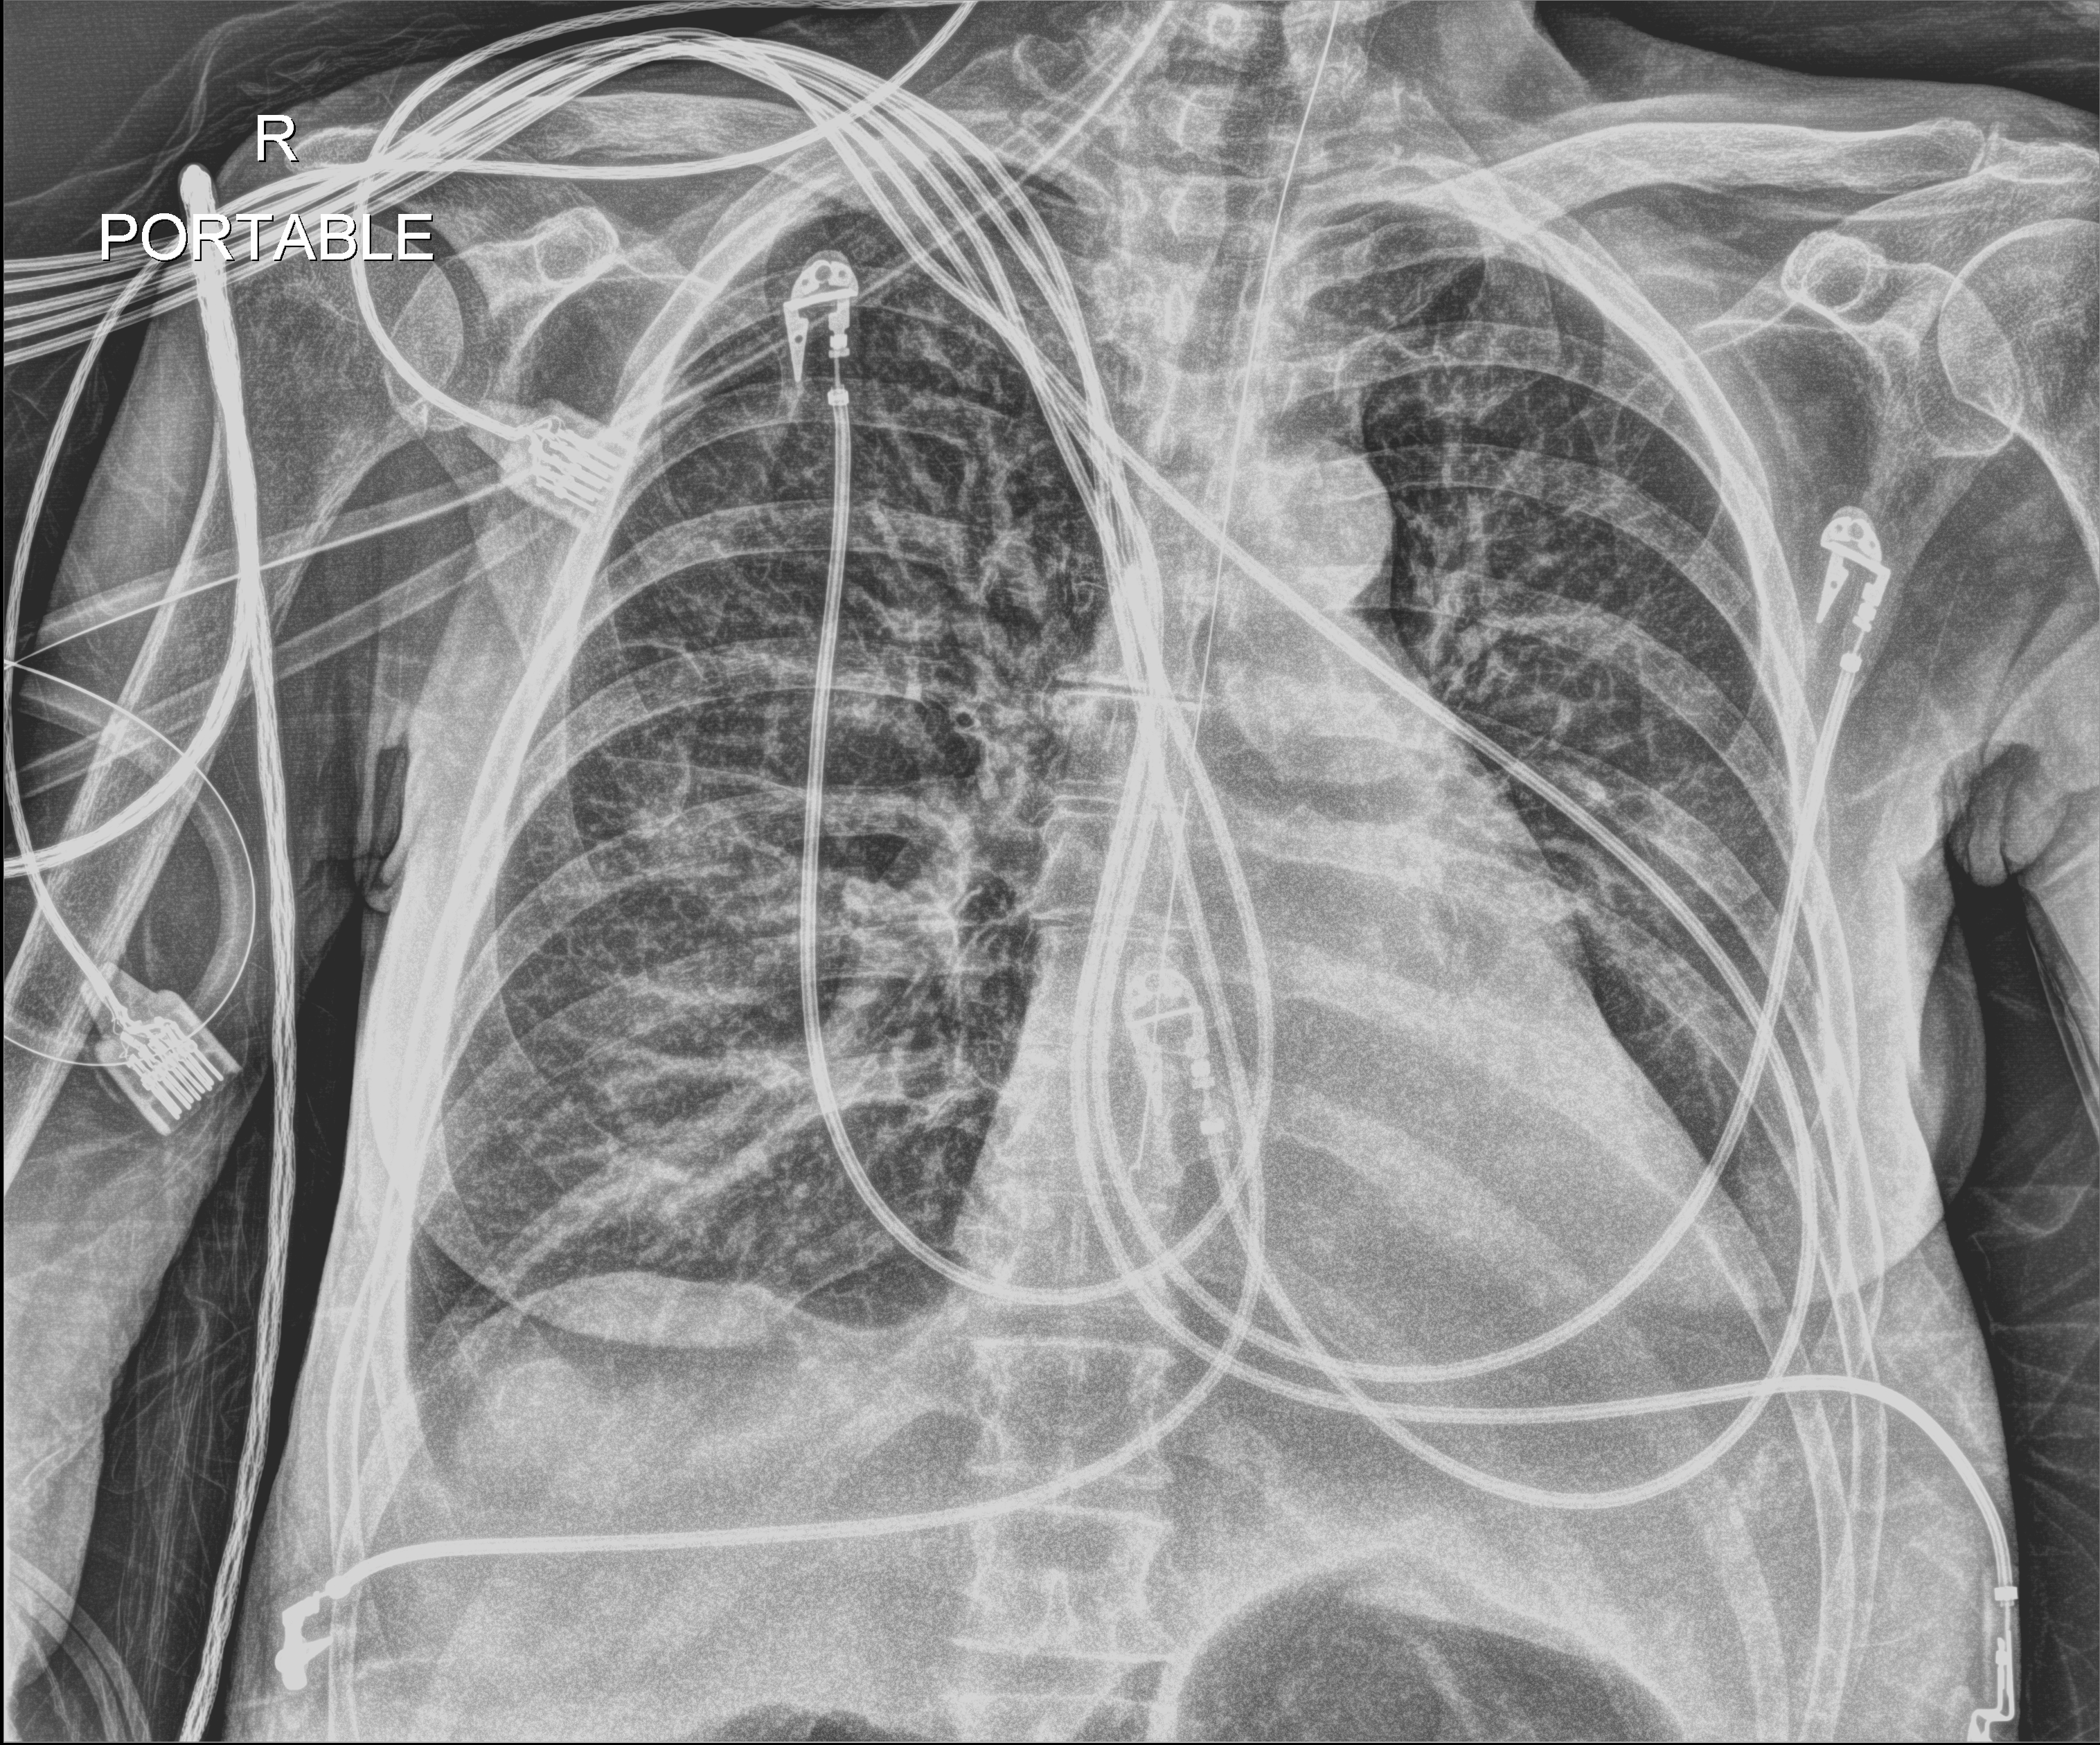
Chest X-ray (portable), anteroposterior (AP) projection. Female patient hospitalised with COVID-19, age 60–74 years.
Hospital-stay facts (about this admission, not read from this image; timing relative to this image not recorded):
- mechanically ventilated during this hospital stay: yes